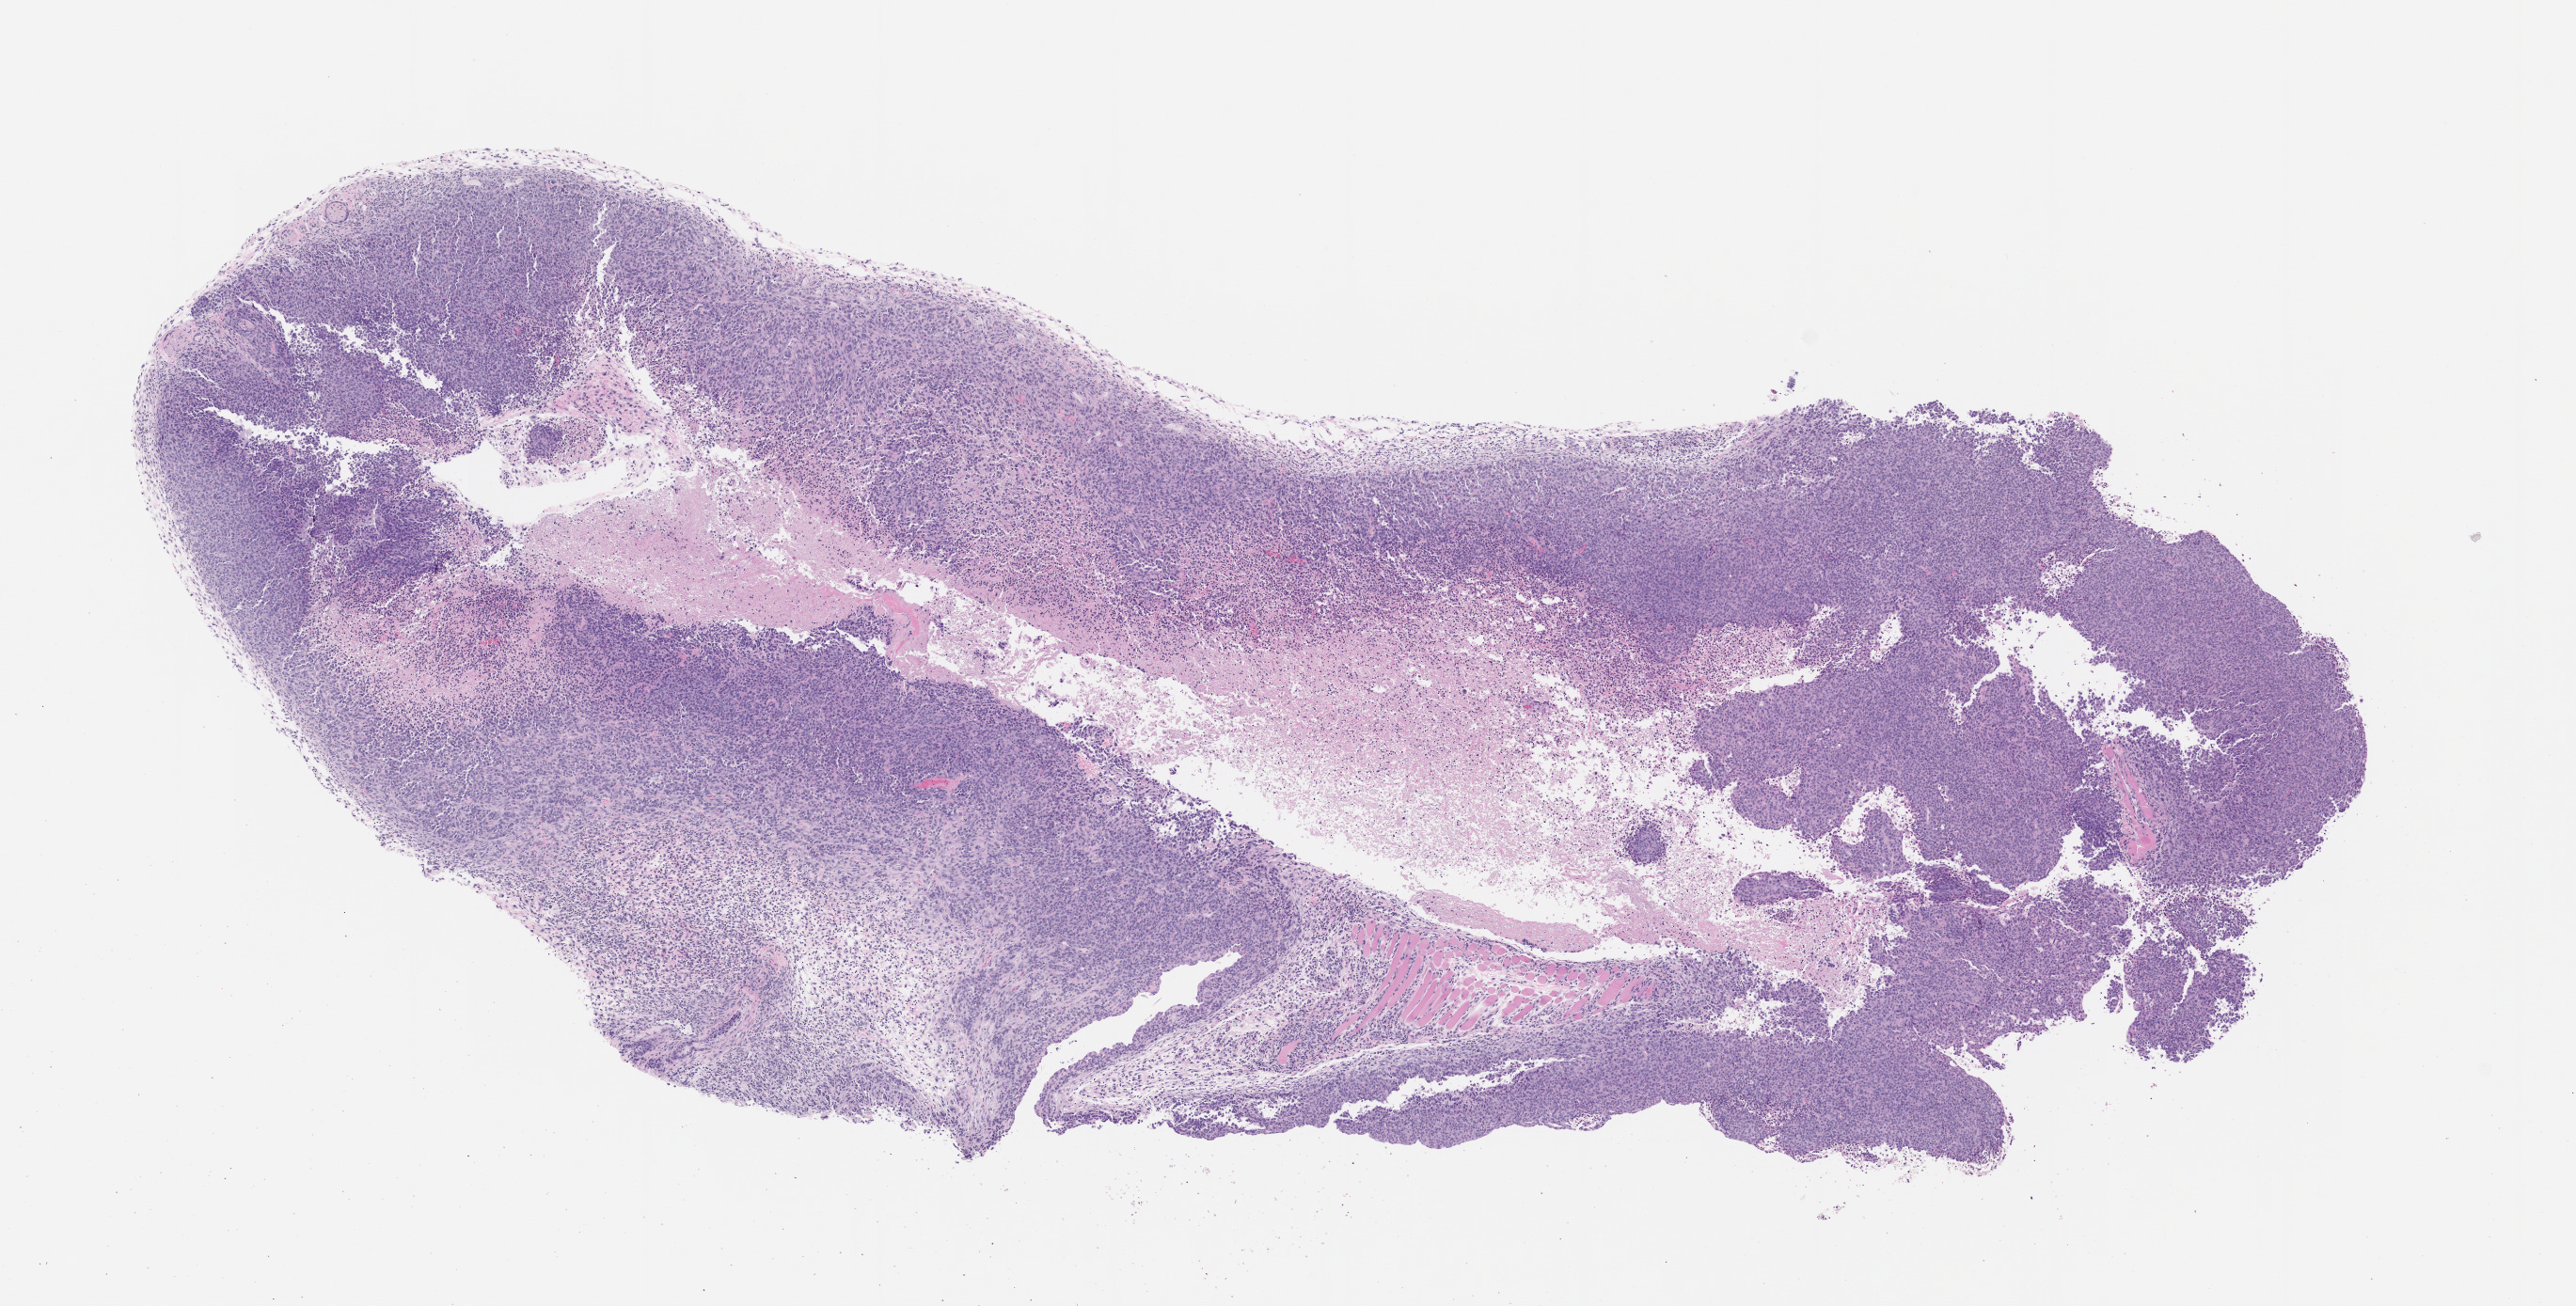
Whole-slide image, hematoxylin and eosin (H&E): patient-derived xenograft (human tumor grown in a mouse), passage 1, low-resolution overview of the scanned area, about 11.0 x 5.6 mm. FFPE section. Tumor site category: pancreas.
Originating patient diagnosis: Pancreatic Adenocarcinoma.